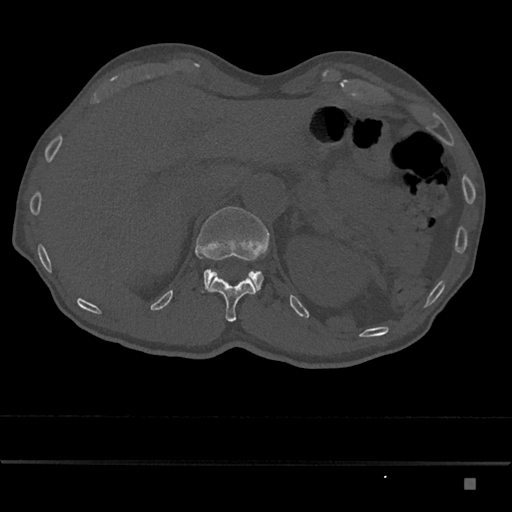
CT including the spine, one axial slice. Position 584 of 797 along the scan axis. Reconstruction kernel Br40s/3. 120 kVp. Bone window (W 1800 / L 400 HU). 0.5 mm slice thickness. 512 × 512 image matrix, field of view 390 × 390 mm. Male patient, age 72 years. From the clinical record (not read from this slice): primary cancer: prostate.
Annotated regions visible in this slice (semi-automatic segmentation, software-assisted and operator-edited):
- L1 vertebra: bounding box [x1, y1, x2, y2] px = [195, 207, 270, 294]
- T12 vertebra: [206, 276, 256, 322]